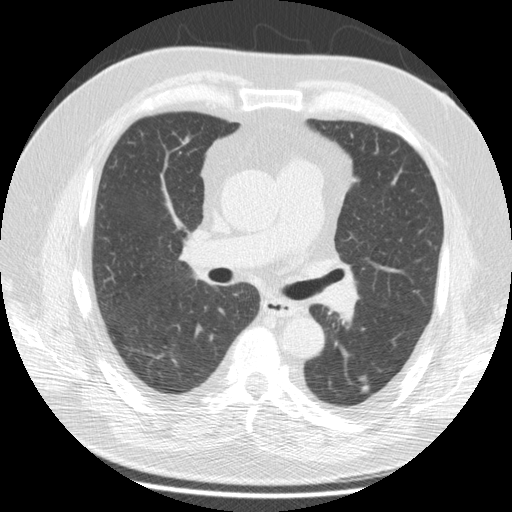
Low-dose screening chest CT, one axial slice; position 101 of 172 along the scan axis; 120 kVp; lung window (W 1500 / L -600 HU); 2.5 mm slice thickness; 512 × 512 image matrix, field of view 364 × 364 mm.
Annotated regions visible in this slice (expert manual segmentation):
- lesion 1 (tumor, lower lobe of left lung): box from (x=361, y=385) to (x=369, y=392) px